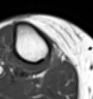
MRI of an extremity soft-tissue mass, one axial slice; position 37 of 54 along the scan axis; MR volume resampled by the dataset authors to the PET/CT grid (not the native acquisition matrix); 3.27 mm slice thickness; 93 × 99 image matrix. Female patient. From the clinical record (not read from this slice): histological type: undifferentiated – high grade; grade: high; site of the primary tumour: right thigh.
Annotated regions visible in this slice (expert contour drawn on MRI and transferred to this co-registered scan by the dataset authors):
- gross tumour volume (mass): bounding box (x1, y1, x2, y2) in pixels: (47, 48, 62, 69)